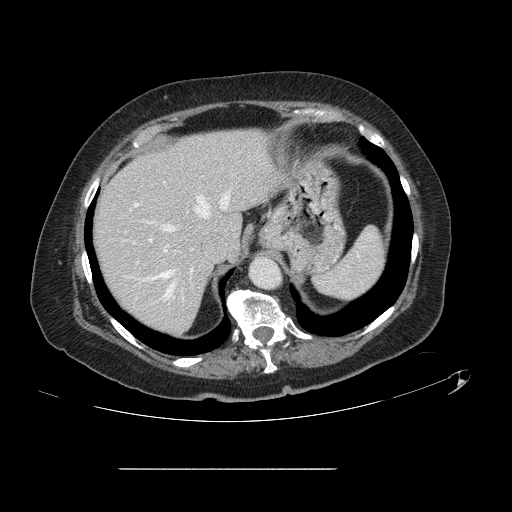
Contrast-enhanced abdominal CT, one axial slice. 120 kVp. Intravenous contrast given. Soft-tissue window (W 400 / L 40 HU). 512 × 512 image matrix, field of view 439 × 439 mm. Female patient, age 75 years. Case-level facts recorded for this patient, not image findings: diagnosis: colorectal cancer liver metastases, imaged before liver resection; multiple liver metastases: no; largest metastasis: 2.4 cm; disease in both lobes: no.
Annotated regions visible in this slice (outlined manually by an expert reader):
- hepatic veins: bounding box (x1, y1, x2, y2) in pixels: (152, 191, 230, 296)
- liver: (92, 130, 281, 334)
- planned liver remnant (the part of the liver to remain after resection): (93, 130, 280, 334)
- portal vein (with intrahepatic branches): (135, 204, 166, 252)